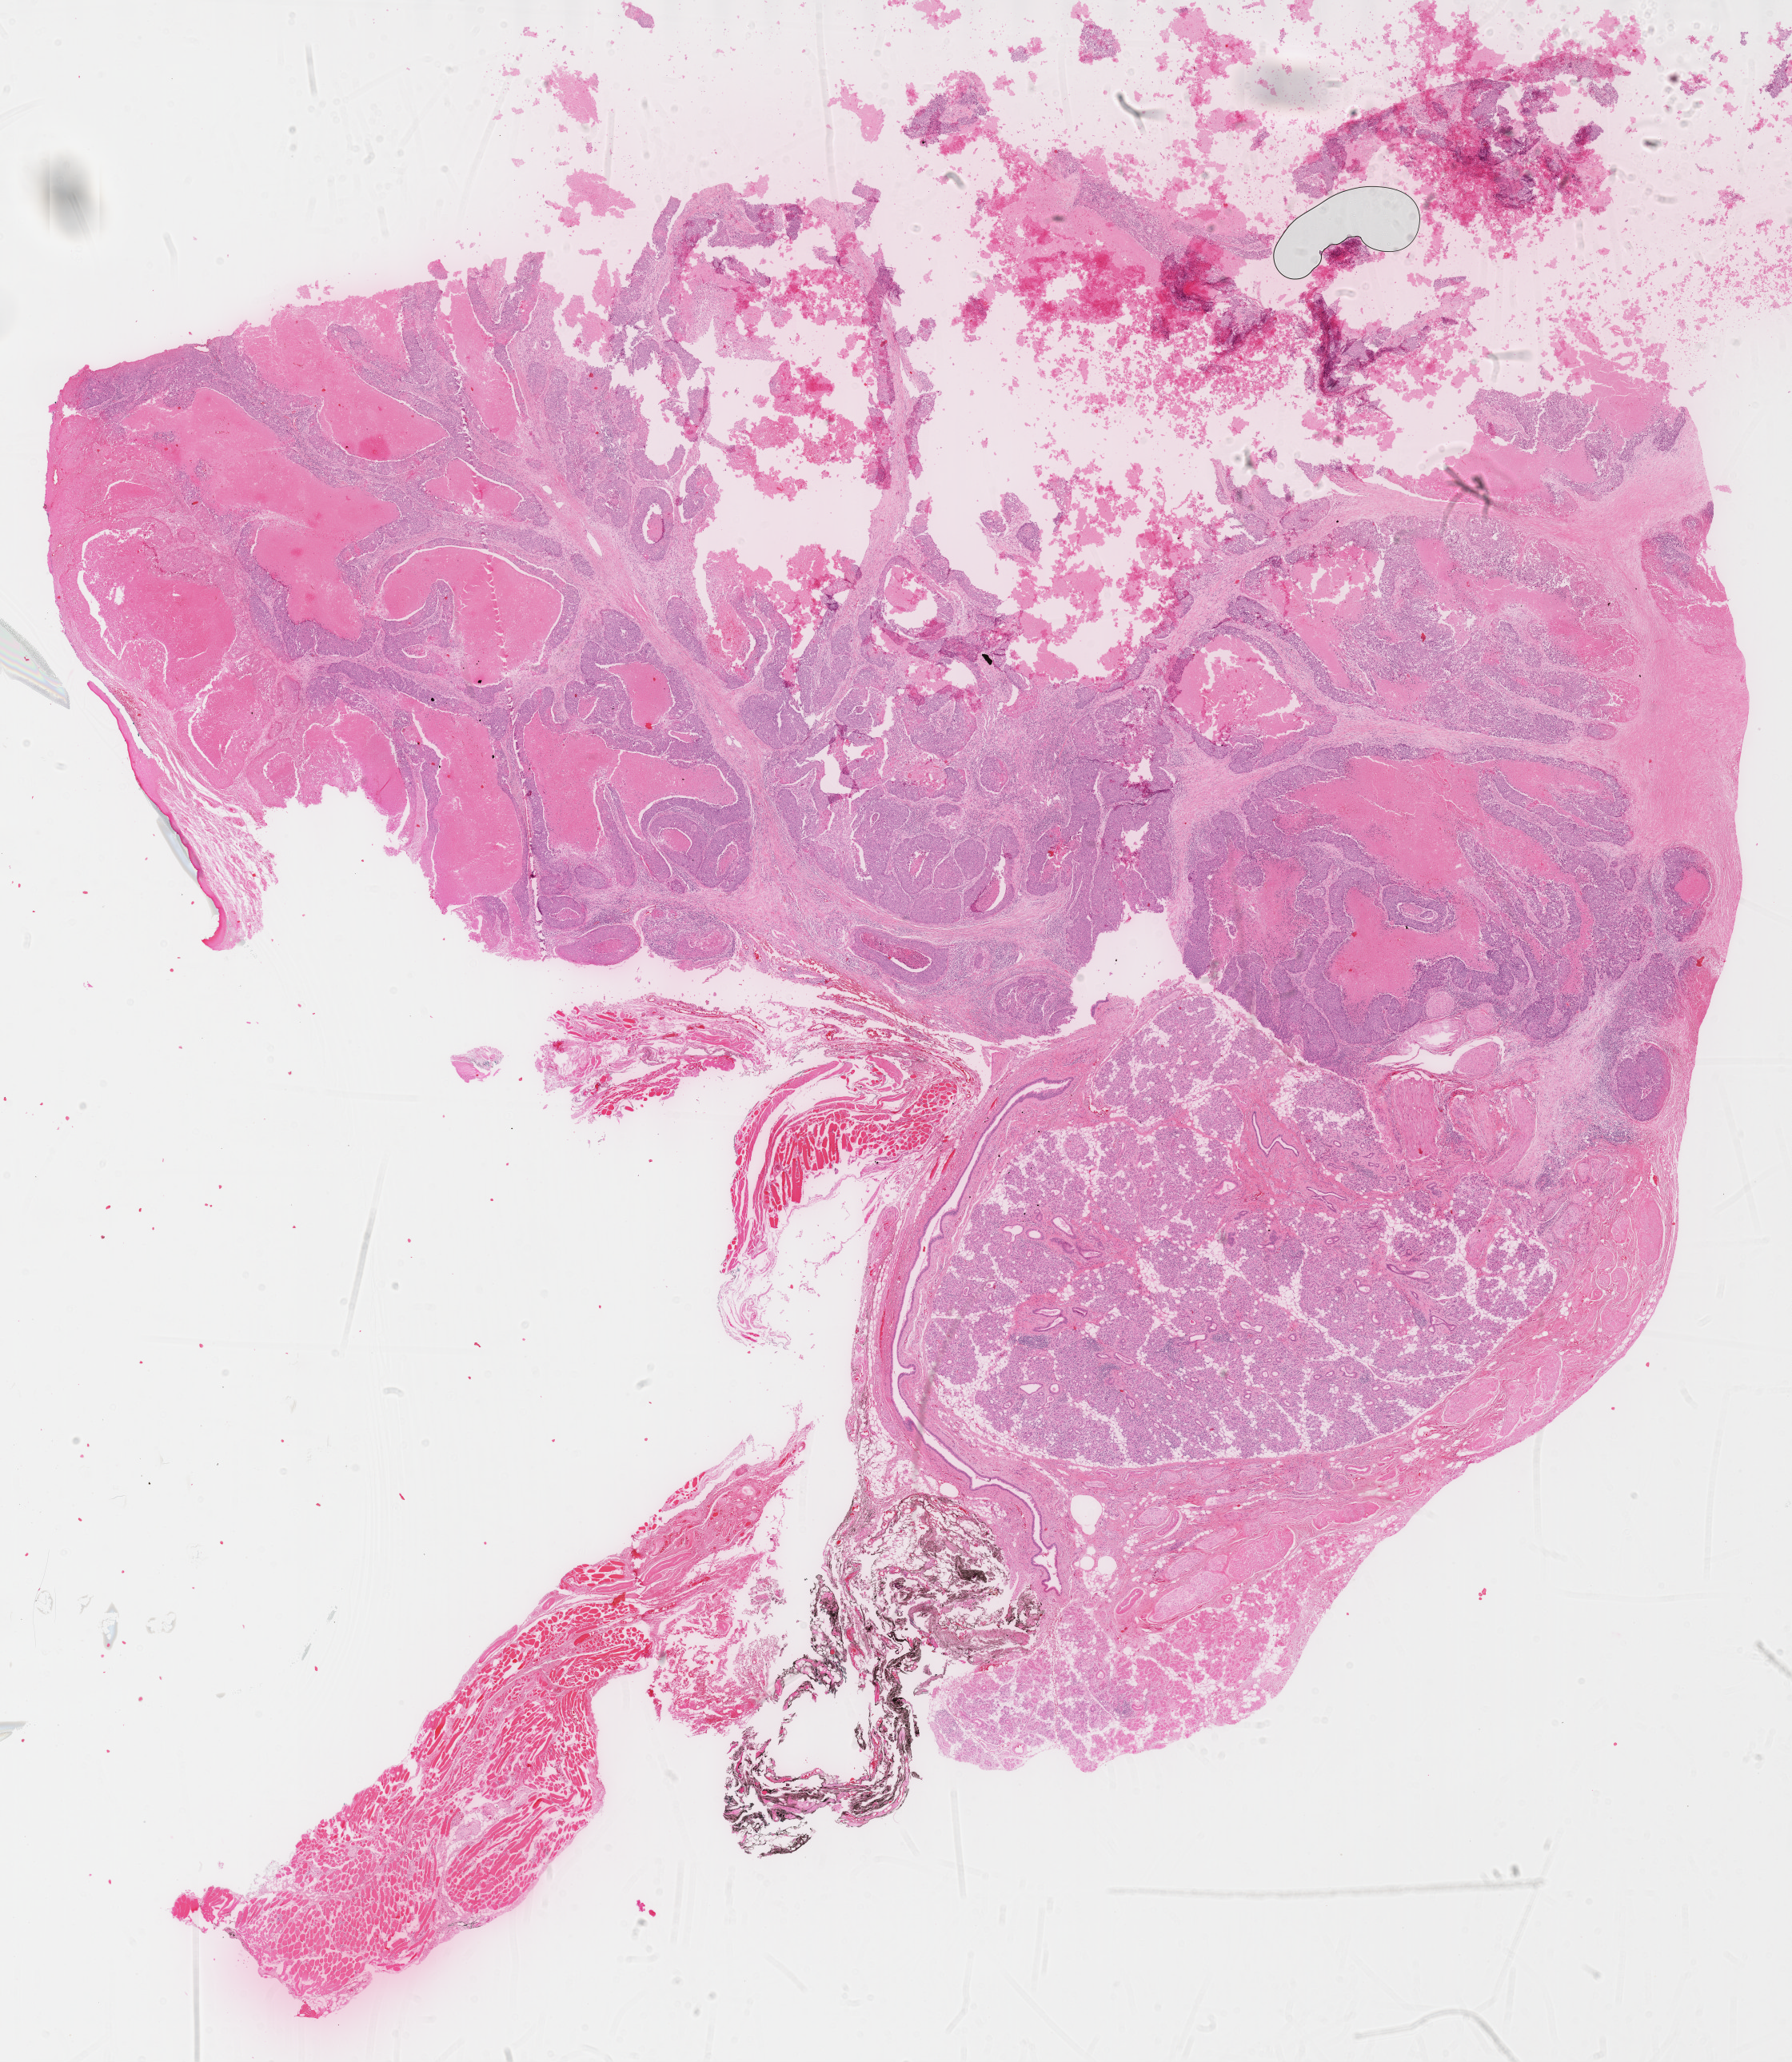
H&E whole-slide image, whole scanned area (about 18.1 x 20.8 mm, slide scanned at 40x) shown as a low-resolution overview; formalin-fixed paraffin-embedded (FFPE) diagnostic section; primary tumour sample from the head and neck. Female, age 79 years at initial diagnosis.
Histologic diagnosis: Squamous cell carcinoma, NOS (floor of mouth, NOS).